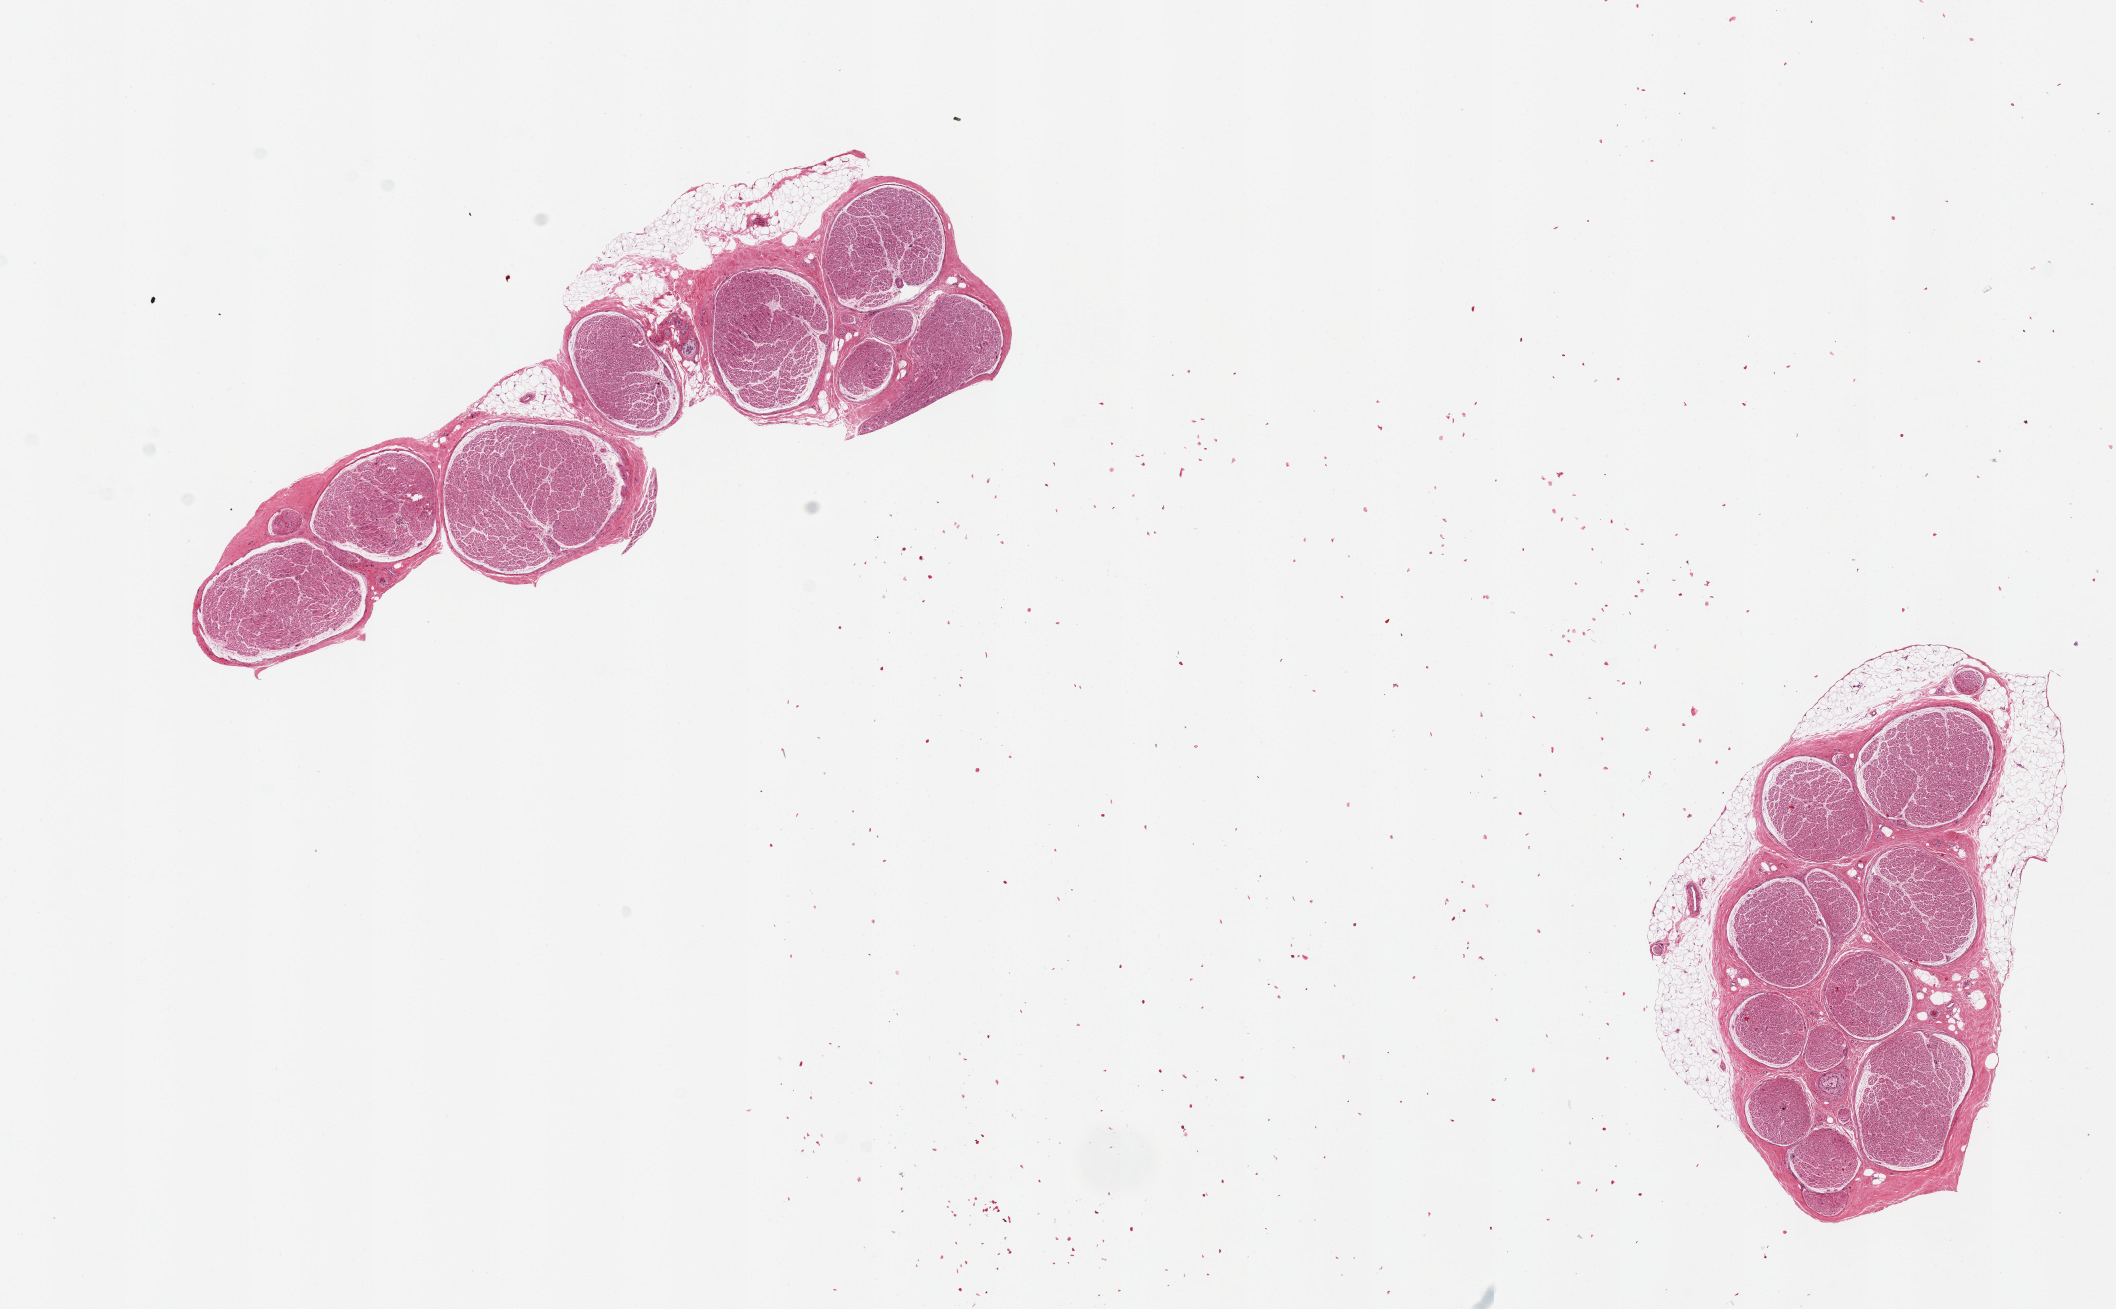
Digitized hematoxylin and eosin (H&E)-stained section — a low-resolution overview of the entire scanned area, about 16.7 x 10.4 mm. PAXgene-fixed, paraffin-embedded tissue. Sampled site (target tissue): tibial nerve. Donor tissue sample. Donor: female.
- reviewer comment on this tissue sample: 2 pieces, discontinuous rim of adherent fat up to ~0.5mm